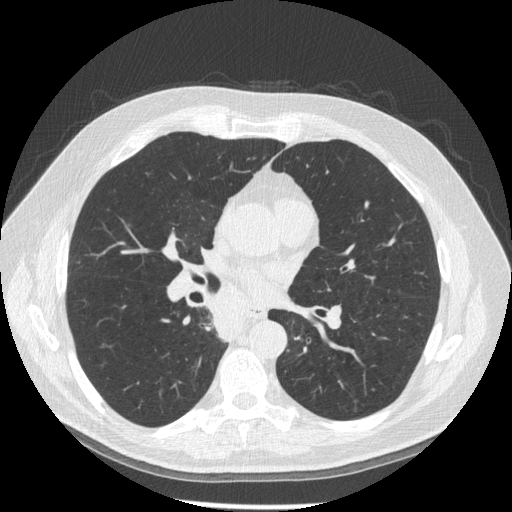
Low-dose screening chest CT, one axial slice. Slice 96 of 181 in the series (ordered by position). Reconstruction kernel STANDARD. 120 kVp. Lung window (W 1500 / L -600 HU). 1.25 mm slice thickness. 512 × 512 image matrix, field of view 370 × 370 mm.
Annotated regions visible in this slice (manually delineated by an expert):
- lesion 1 (tumor, lower lobe of right lung): bounding box [x1, y1, x2, y2] px = [210, 297, 244, 342]